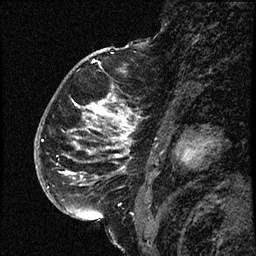
Breast MRI (dynamic contrast-enhanced), one sagittal slice. Slice 43 of 66 in the series (ordered by position). Dynamic contrast-enhanced study with each time point stored as its own series, time point 2 of 3 at this slice position (early post-contrast, ordered by acquisition time). 1.5 T. TE 4.2 ms, TR 17.6 ms. 2 mm slice thickness. 256 × 256 image matrix, field of view 200 × 200 mm. Female patient. Case-level facts recorded for this patient, not image findings: setting: breast cancer imaged before/during neoadjuvant chemotherapy; receptor status: HER2-positive.
Structures marked on this image (semi-automatic segmentation, software-assisted and operator-edited):
- analysis volume of interest (the breast-tissue region the enhancement analysis was run in; not a lesion): bounding box (x1, y1, x2, y2) in pixels: (52, 69, 145, 209)
- tumour enhancement mask (voxels above the 100 % enhancement threshold inside the analysis volume of interest): (65, 85, 131, 209)